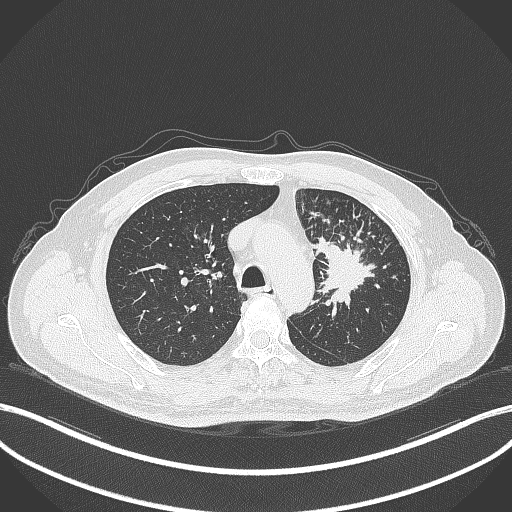
Chest CT, one axial slice. Slice 261 of 386 in the series (ordered by position). Reconstruction kernel B70f. 120 kVp. Lung window (W 1500 / L -600 HU). 1 mm slice thickness. 512 × 512 image matrix, field of view 400 × 400 mm. Male patient, age 69 years. Case-level facts recorded for this patient, not image findings: clinical TNM (as recorded): T2a N2 M0; histopathological grade: G2-3.
Outlined on this slice (rectangle marked by the reading radiologist):
- lung tumour (recorded histology: adenocarcinoma): box from (x=312, y=233) to (x=377, y=314) px